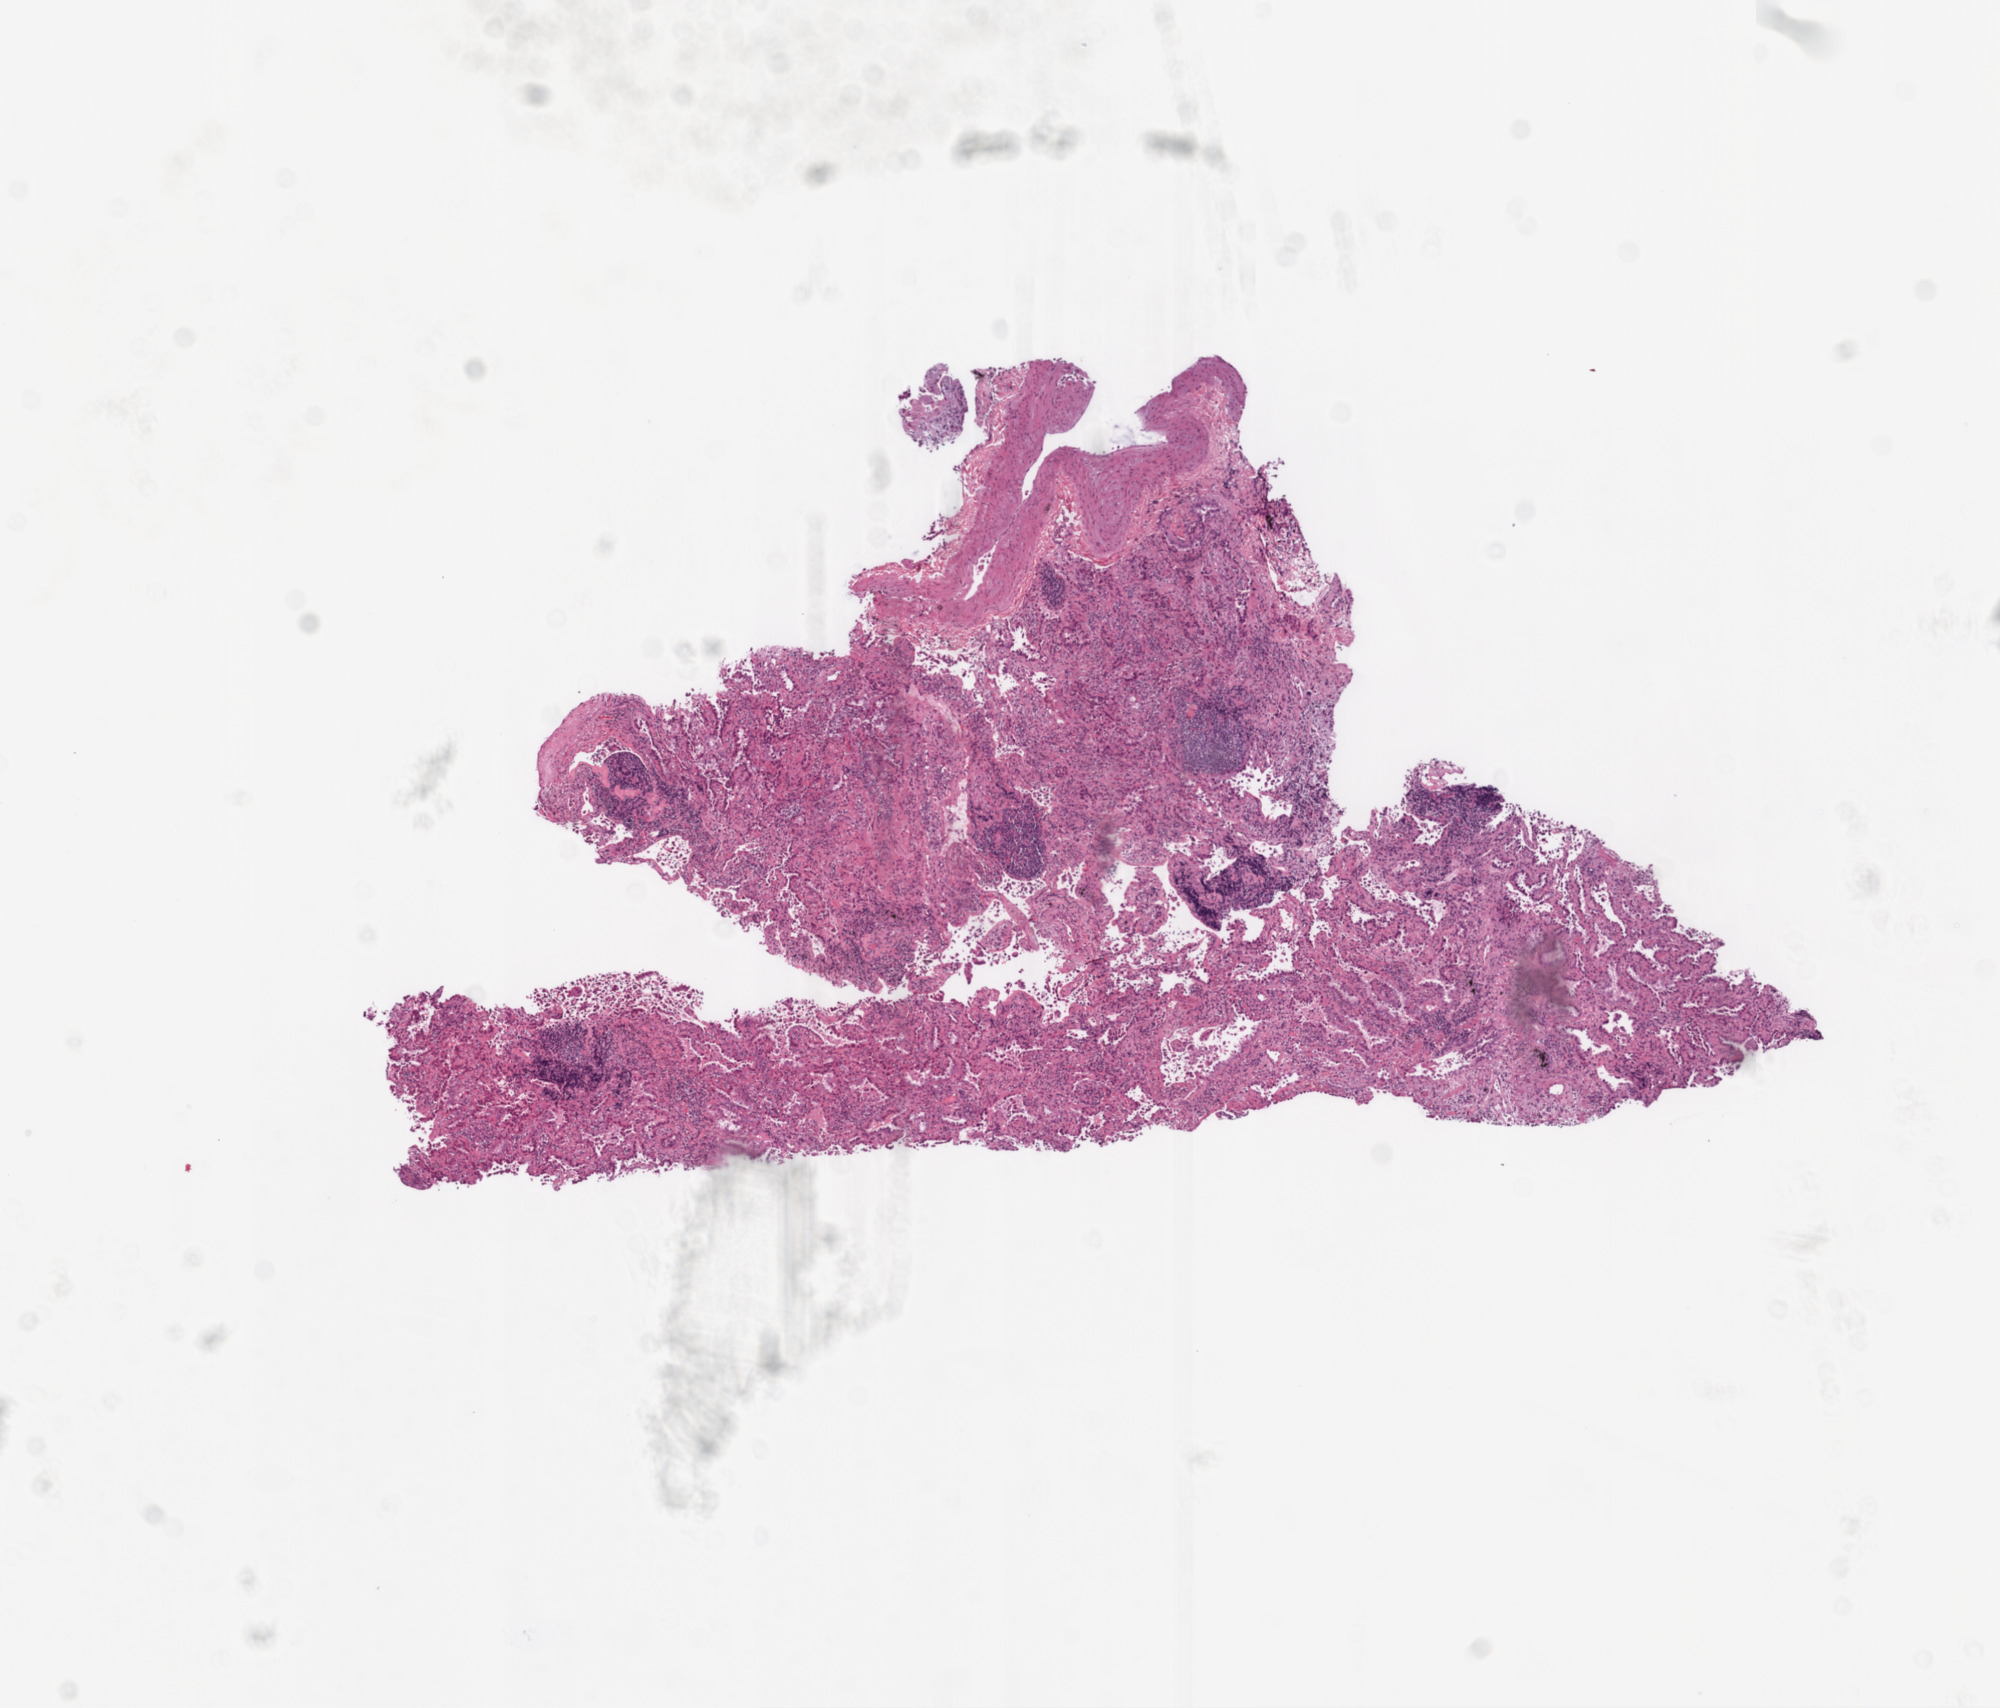
H&E whole-slide image — a low-resolution overview of the entire scanned area, about 8.0 x 6.9 mm (slide scanned at 20x). Frozen section from the top of the tissue portion. Primary tumour sample from the lung. Patient: female, age at initial diagnosis 74 years. Slide review estimates, as recorded: tumour cells 80%, tumour nuclei 70%, normal cells 5%, stromal cells 15%, necrosis 0%. Inflammatory infiltration, as recorded: lymphocyte infiltration 5%.
- AJCC pathologic stage: IB (6th edition)
- histologic diagnosis: Adenocarcinoma, NOS (upper lobe, lung)